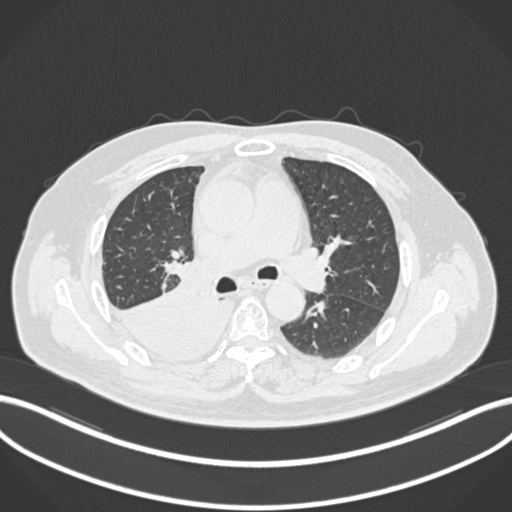
Chest CT, one axial slice. Position 118 of 218 along the scan axis. Reconstruction kernel B30f. Lung window (W 1500 / L -600 HU). 512 × 512 image matrix, field of view 400 × 400 mm. Patient: male, 68 years. Case-level facts recorded for this patient, not image findings: clinical TNM (as recorded): T2a N0 M0.
Structures marked on this image (rectangle marked by the reading radiologist):
- lung tumour (recorded histology: adenocarcinoma): bounding box [x1, y1, x2, y2] px = [110, 287, 235, 362]